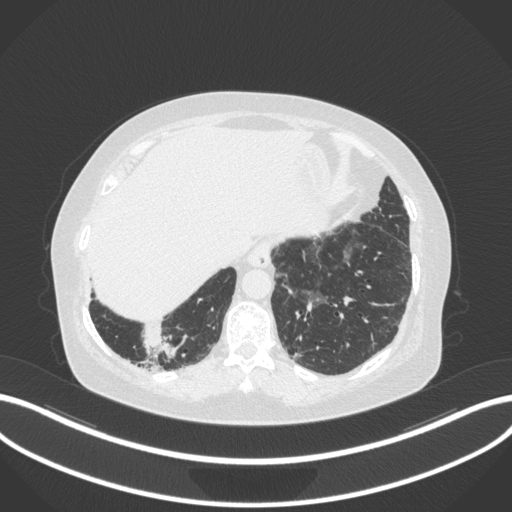
Chest CT, one axial slice; slice 22 of 303 in the series (ordered by position); reconstruction kernel B31f; lung window (W 1500 / L -600 HU); 1 mm slice thickness; 512 × 512 image matrix, field of view 400 × 400 mm. Patient: female, 65 years. Case-level facts recorded for this patient, not image findings: clinical TNM (as recorded): T2b N1 M0; histopathological grade: G1.
Structures marked on this image (rectangle marked by the reading radiologist):
- lung tumour (recorded histology: adenocarcinoma): bounding box (x1, y1, x2, y2) in pixels: (133, 326, 179, 360)